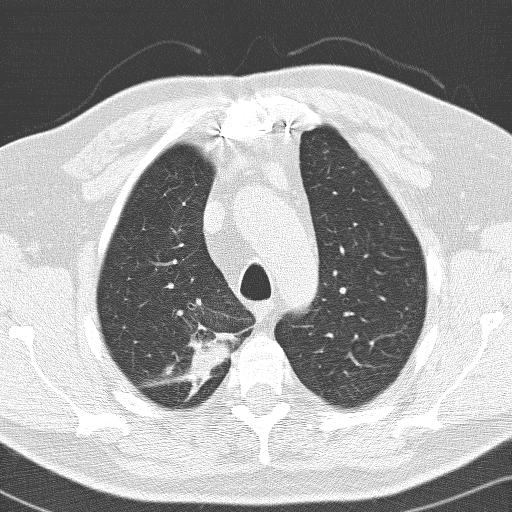
Low-dose screening chest CT, axial slice. Baseline screening round. Lung window (W 1500 / L -600 HU). 3.2 mm slice thickness. Lung (sharp) reconstruction kernel (D). Slice 28 of 141 in the series. 512 × 512 image matrix, field of view 326 × 326 mm. Male participant, aged 66 years at enrolment. Former smoker at enrolment.
- Expert-annotated lung lesion, bounding box <153,314,231,394> (left, top, right, bottom; pixels).
- The exam's reader record, not a measurement of the box and not confirmed to be the same lesion: non-calcified nodule or mass ≥4 mm, right upper lobe, 36 × 30 mm, spiculated (stellate) margins, soft tissue attenuation.
- Official screen result: positive, change unspecified: nodule(s) >= 4 mm or enlarging nodule(s), mass(es), or other non-specific abnormalities suspicious for lung cancer.
- Later outcome: lung cancer diagnosed 103 days after this screen — adenocarcinoma, NOS, right upper lobe, poorly differentiated (G3), stage IIB (AJCC 6th edition), 33 mm at pathology.